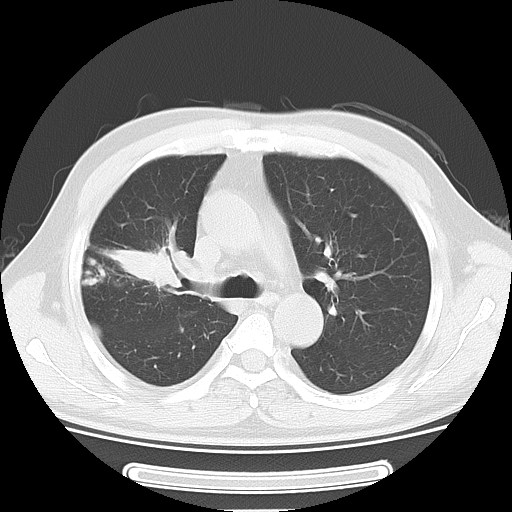
Chest CT, one axial slice. Reconstruction kernel LUNG. 120 kVp. Lung window (W 1500 / L -600 HU). 5 mm slice thickness. 512 × 512 image matrix, field of view 350 × 350 mm. Patient: male, 46 years. From the clinical record (not read from this slice): clinical TNM (as recorded): T3 N0 M1b.
Structures marked on this image (bounding box drawn by a radiologist):
- lung tumour (recorded histology: adenocarcinoma): bounding box (x1, y1, x2, y2) in pixels: (89, 228, 192, 315)